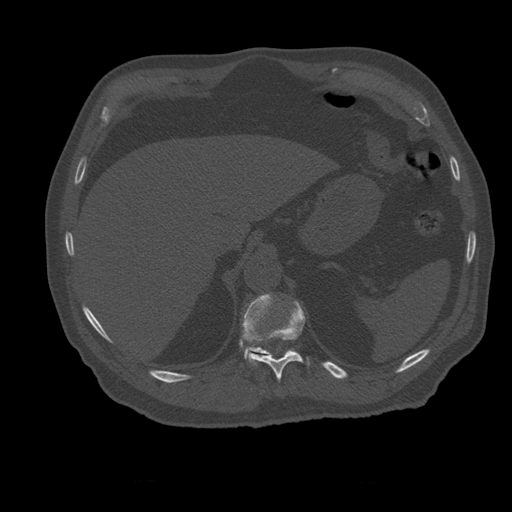
CT including the spine, one axial slice. Slice 277 of 399 in the series (ordered by position). Reconstruction kernel STANDARD. 120 kVp. Bone window (W 1800 / L 400 HU). 1.25 mm slice thickness. 512 × 512 image matrix, field of view 407 × 407 mm. Patient age 73 years. Case-level facts recorded for this patient, not image findings: primary cancer: prostate.
Outlined on this slice (semi-automatically segmented with operator editing):
- T11 vertebra: bounding box [x1, y1, x2, y2] px = [249, 302, 310, 381]
- T12 vertebra: [240, 294, 296, 360]